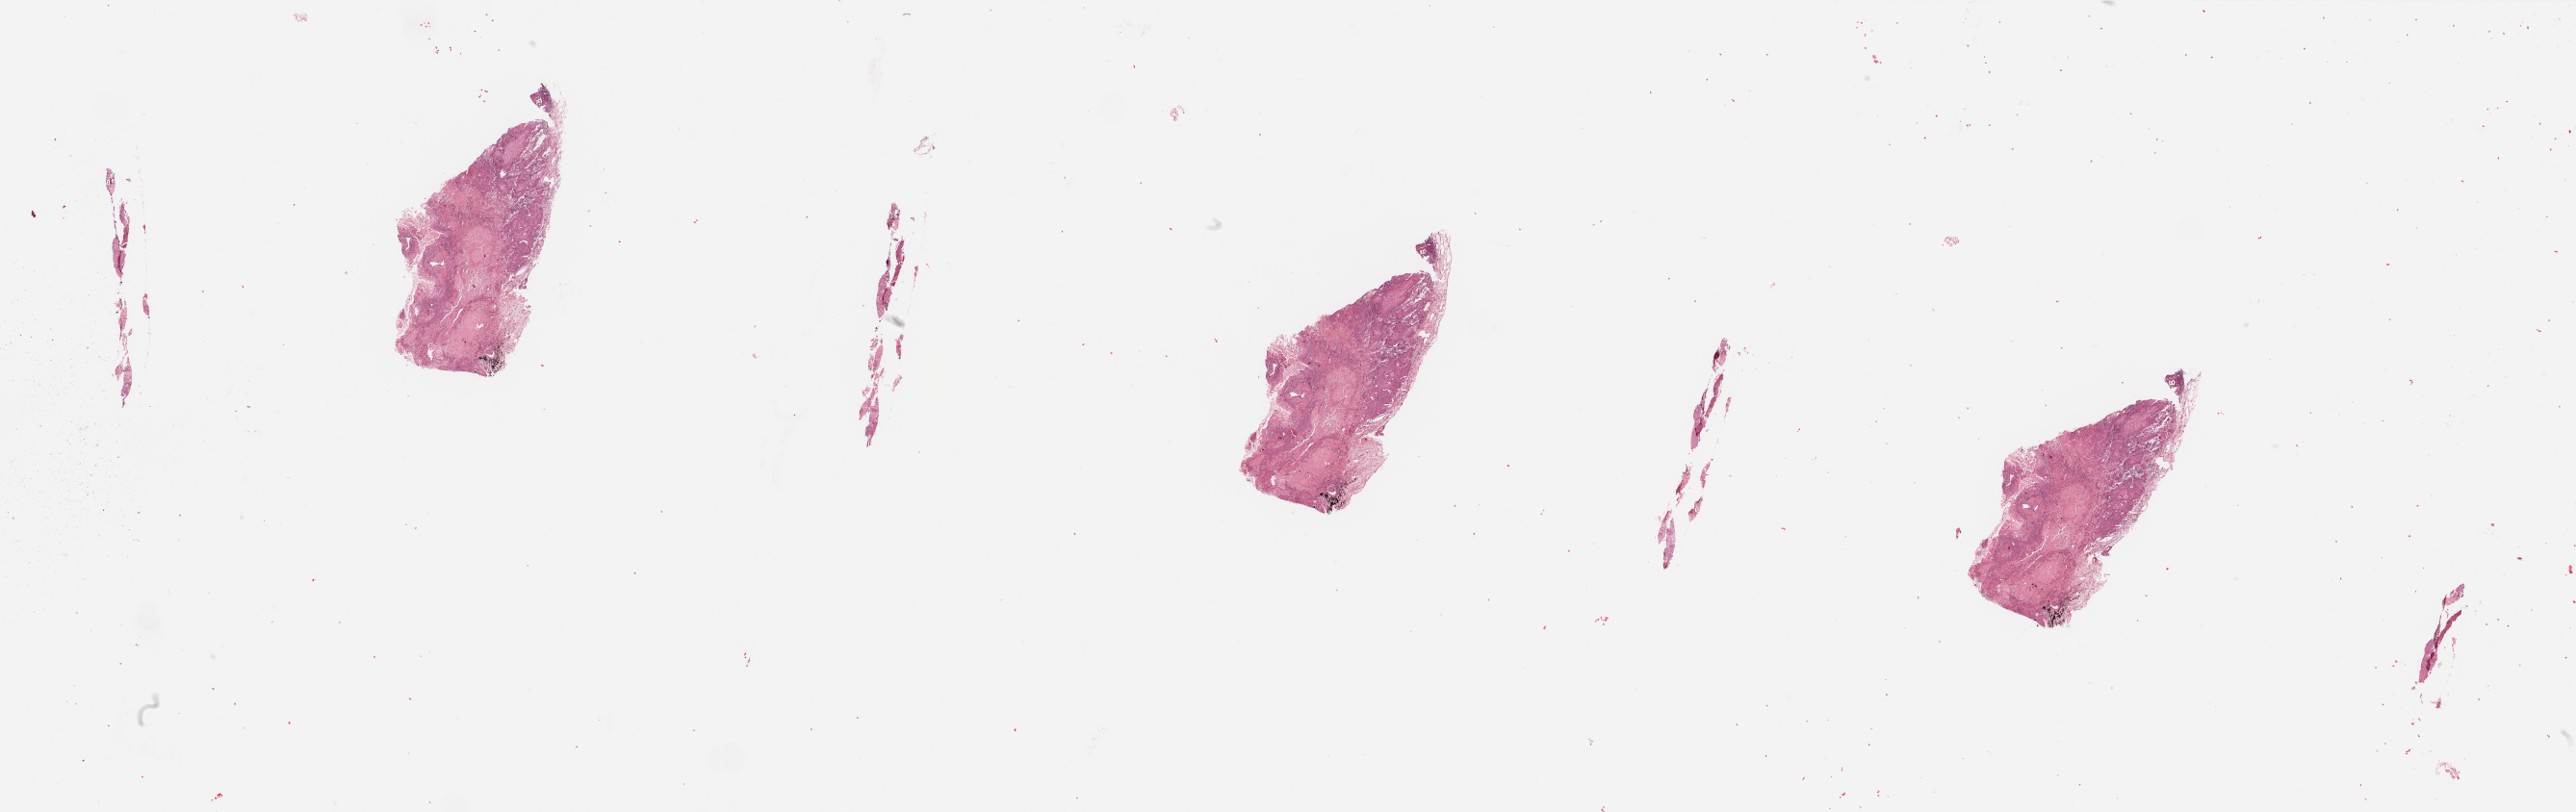
H&E whole-slide image — shown as a low-resolution overview of the whole scanned area (about 42.3 x 13.4 mm, slide scanned at 20x). Tumour tissue sample, sampled site: lung. Patient: male, age 69 years. Histologic grade: G2 (moderately differentiated). Composition of this section per pathologist review: tumour nuclei 70%, necrosis 20%.
AJCC pathologic stage: IIIA. Diagnosis: Squamous cell carcinoma, NOS. Primary tumour site (as recorded): right upper lobe.